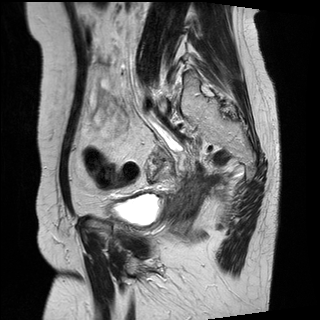
Pelvic MRI for cervical cancer, one sagittal slice. Slice 7 of 27 in the series (ordered by position). T2-weighted. 1.5 T. TE 89 ms, TR 2740 ms. 4 mm slice thickness. 320 × 320 image matrix, field of view 260 × 260 mm. Patient: female, 42 years.
Outlined on this slice (manually delineated by an expert):
- uterus and cervix: box from (x=173, y=179) to (x=206, y=208) px